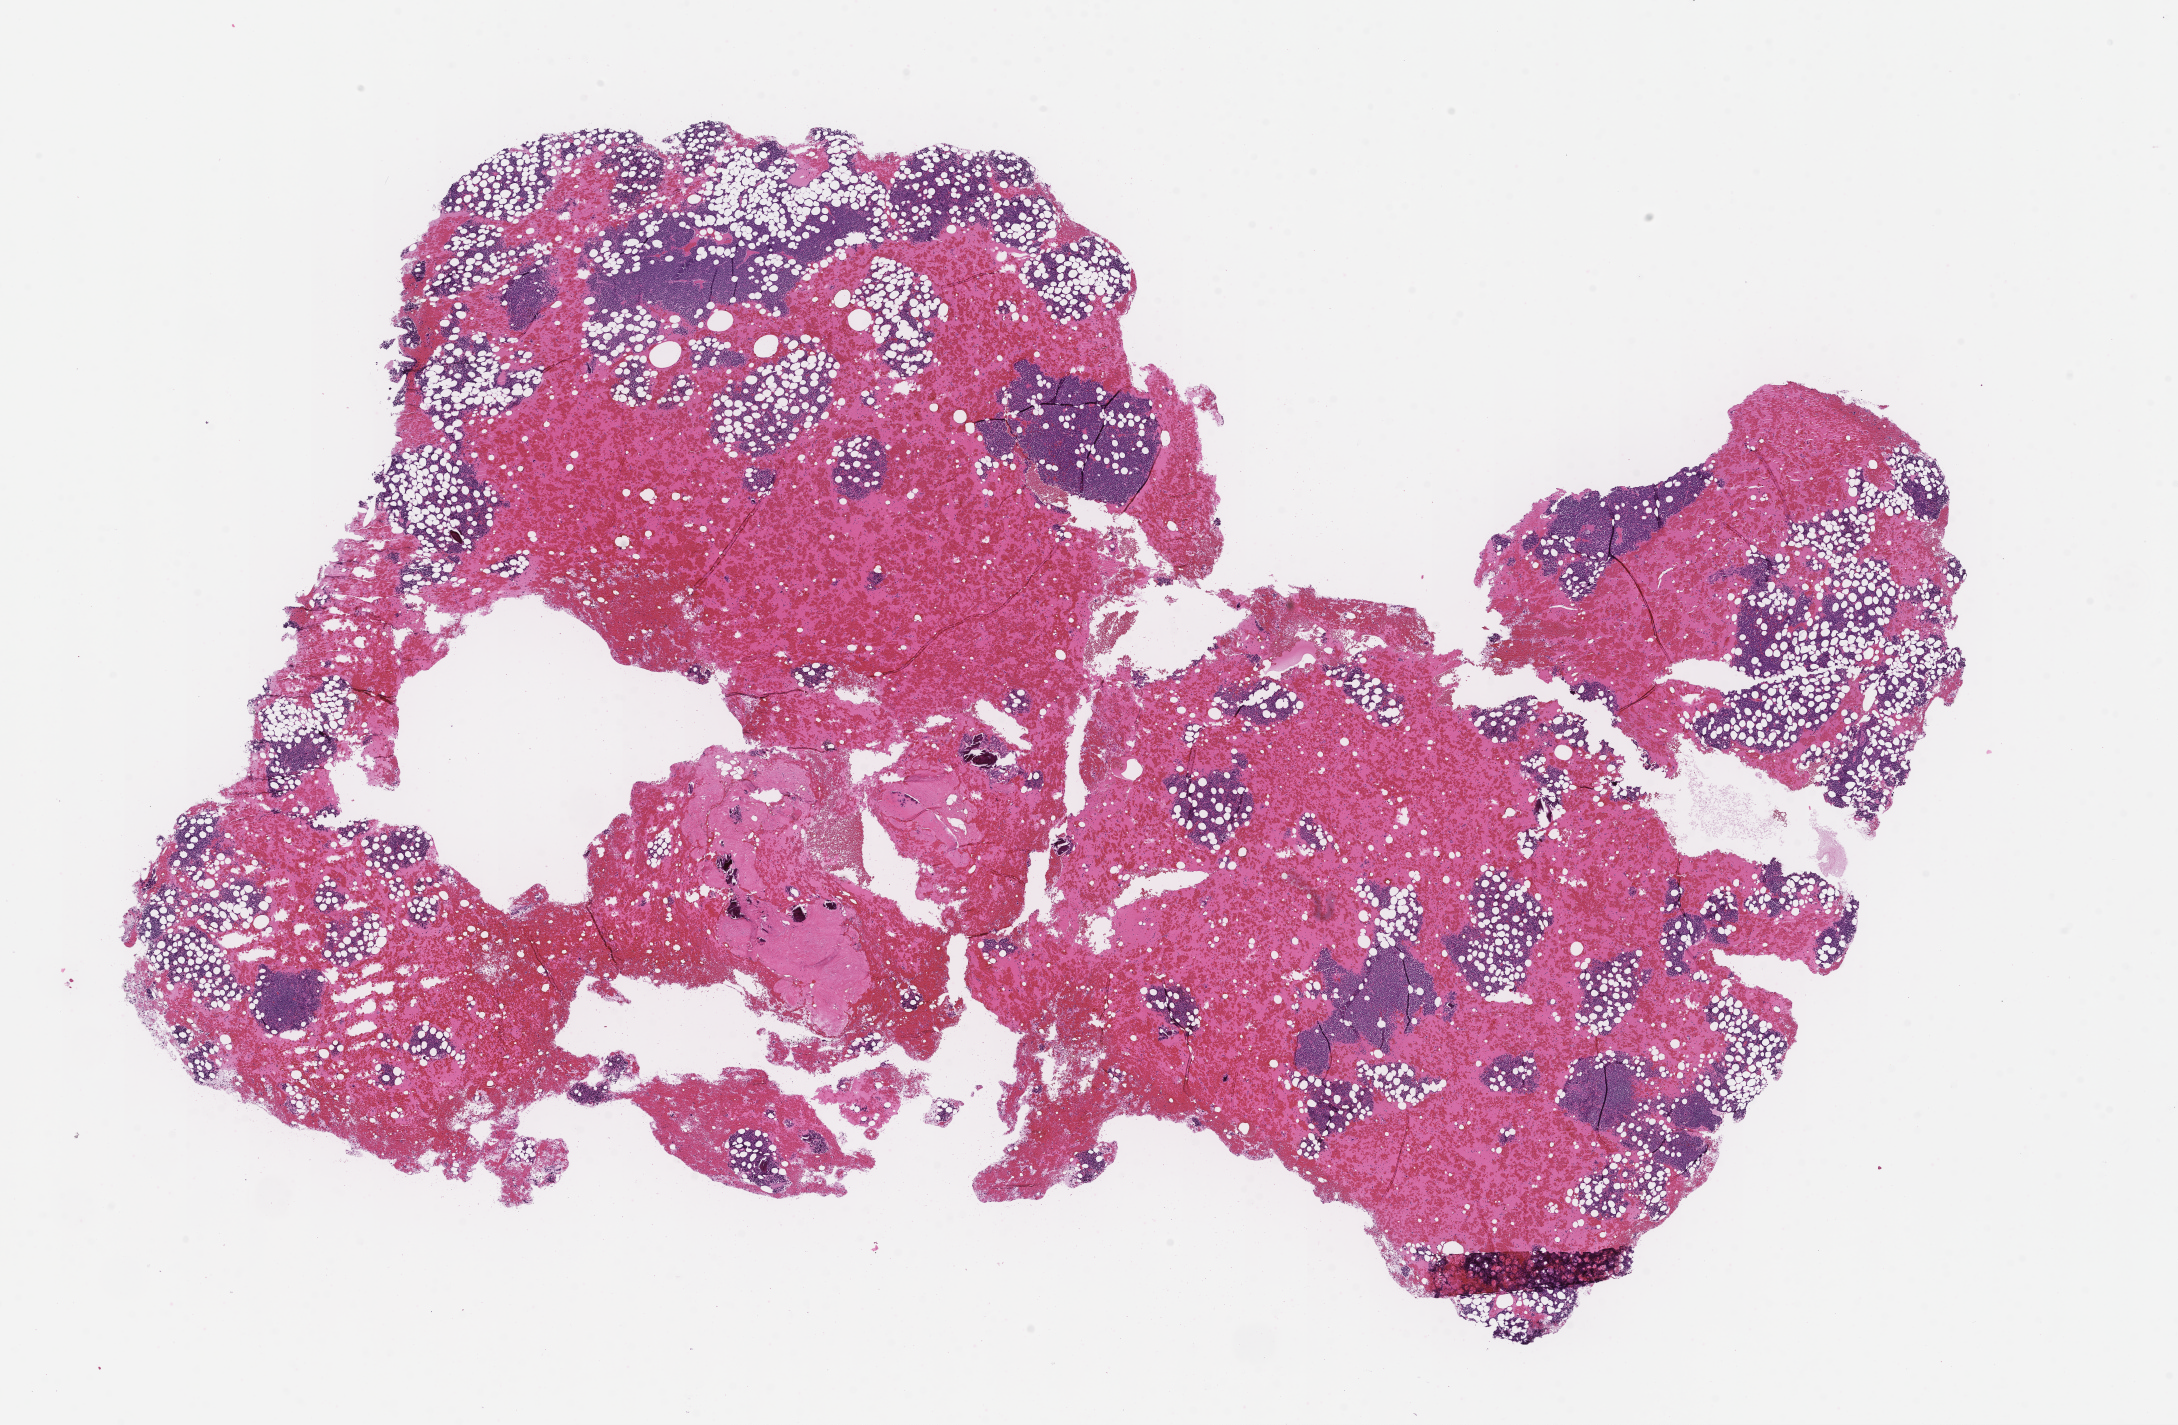
Whole-slide image, H&E stain — shown as a low-resolution overview of the whole scanned area (about 17.6 x 11.5 mm); FFPE section; site: bone marrow; specimen time point: archival tissue. Patient sex: male.
This section: primary tumor. Diagnosis: Plasma Cell Myeloma.